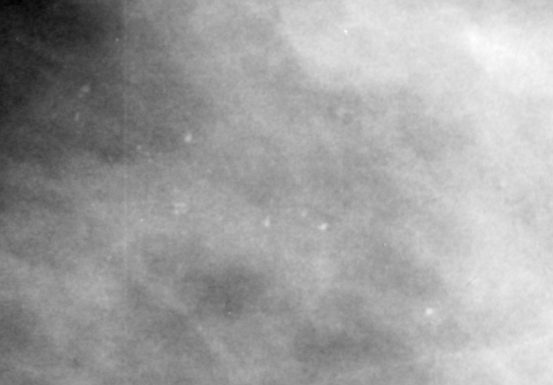
Crop from a digitized film mammogram around one marked abnormality; left breast; CC view; BI-RADS breast density category 4 (scale 1–4).
Marked abnormality: calcifications, morphology amorphous, distribution clustered; BI-RADS assessment category 4; pathology result (as recorded, not read from the image): malignant.